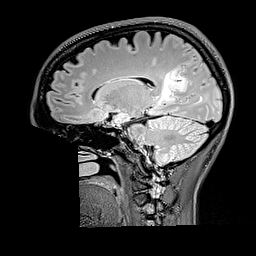
Brain MRI from a brain-tumour surgery series, one sagittal slice; position 101 of 176 along the scan axis; T2 FLAIR; 1 mm slice thickness; 256 × 256 image matrix, field of view 256 × 256 mm. From the clinical record (not read from this slice): histopathology: Oligodendroglioma; WHO grade: 2.
Annotated regions visible in this slice (outlined manually by an expert reader):
- tumour: bounding box <158,64,187,104> (left, top, right, bottom; pixels)